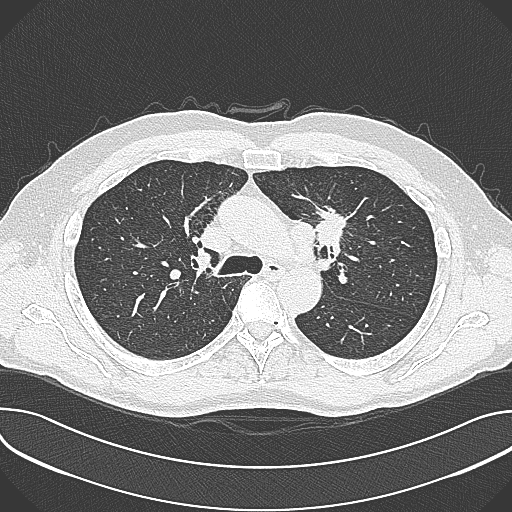
Low-dose screening chest CT, axial slice, baseline annual screen, lung window (W 1500 / L -600 HU), 1 mm slice thickness, lung (sharp) reconstruction kernel (B80f), slice 107 of 361 in the series, 512 × 512 image matrix. Male, age 59 years at enrolment. Current smoker at enrolment.
Expert-annotated lung lesion, box from (x=302, y=195) to (x=362, y=256) px. The screening reader recorded 2 non-calcified nodules or masses ≥4 mm on this exam; which of them this box marks is not recorded. Lung cancer was diagnosed 21 days after this screen: non-small cell carcinoma, left upper lobe, poorly differentiated (G3), stage IIIA (AJCC 6th edition), 35 mm at pathology.